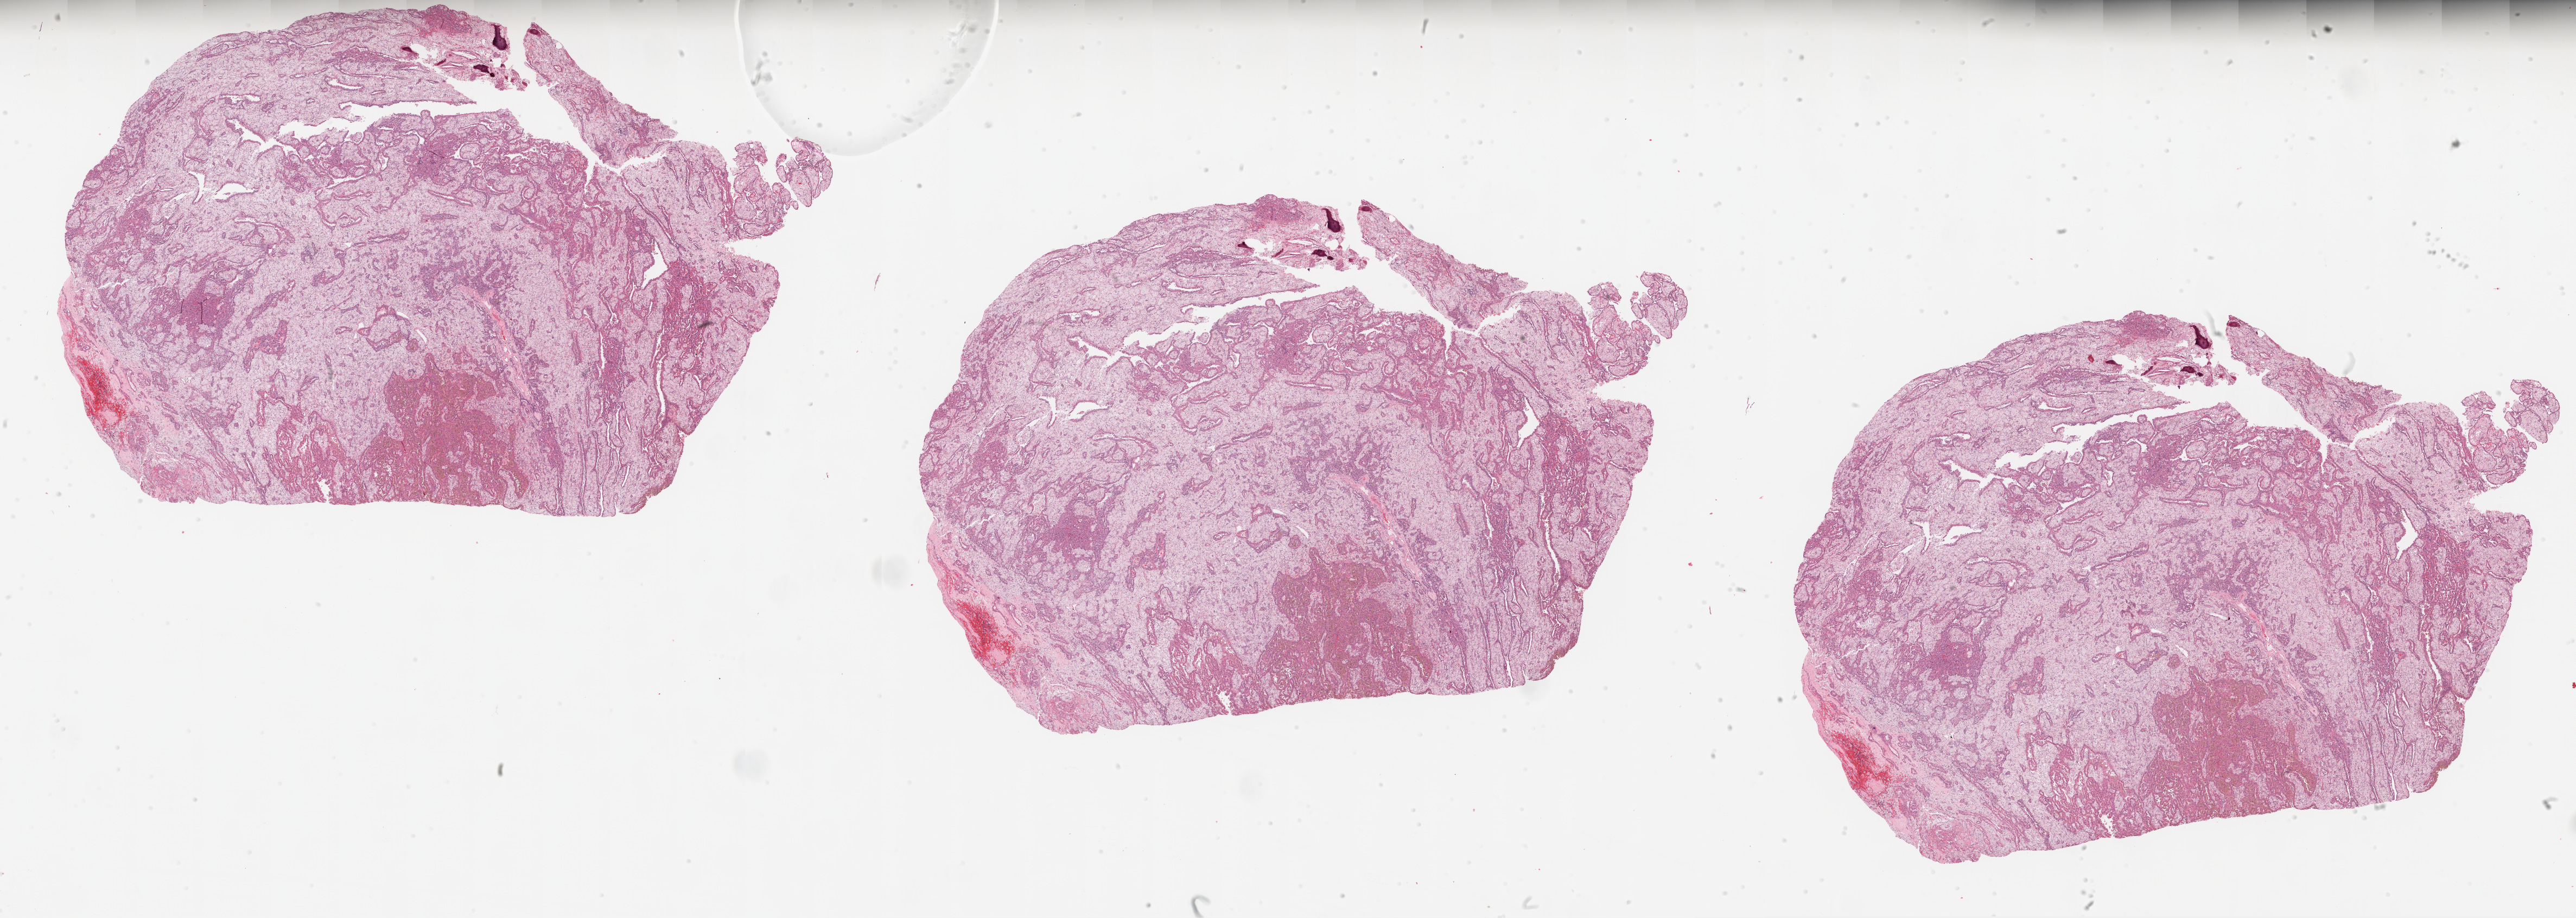
Digitized H&E tissue section (whole slide) — low-resolution overview of the scanned area, about 38.0 x 13.5 mm (from a 20x scan); formalin-fixed paraffin-embedded (FFPE) diagnostic section; primary tumour sample from the kidney. Patient sex: male.
AJCC pathologic stage: I. Pathologic diagnosis: Papillary adenocarcinoma, NOS.